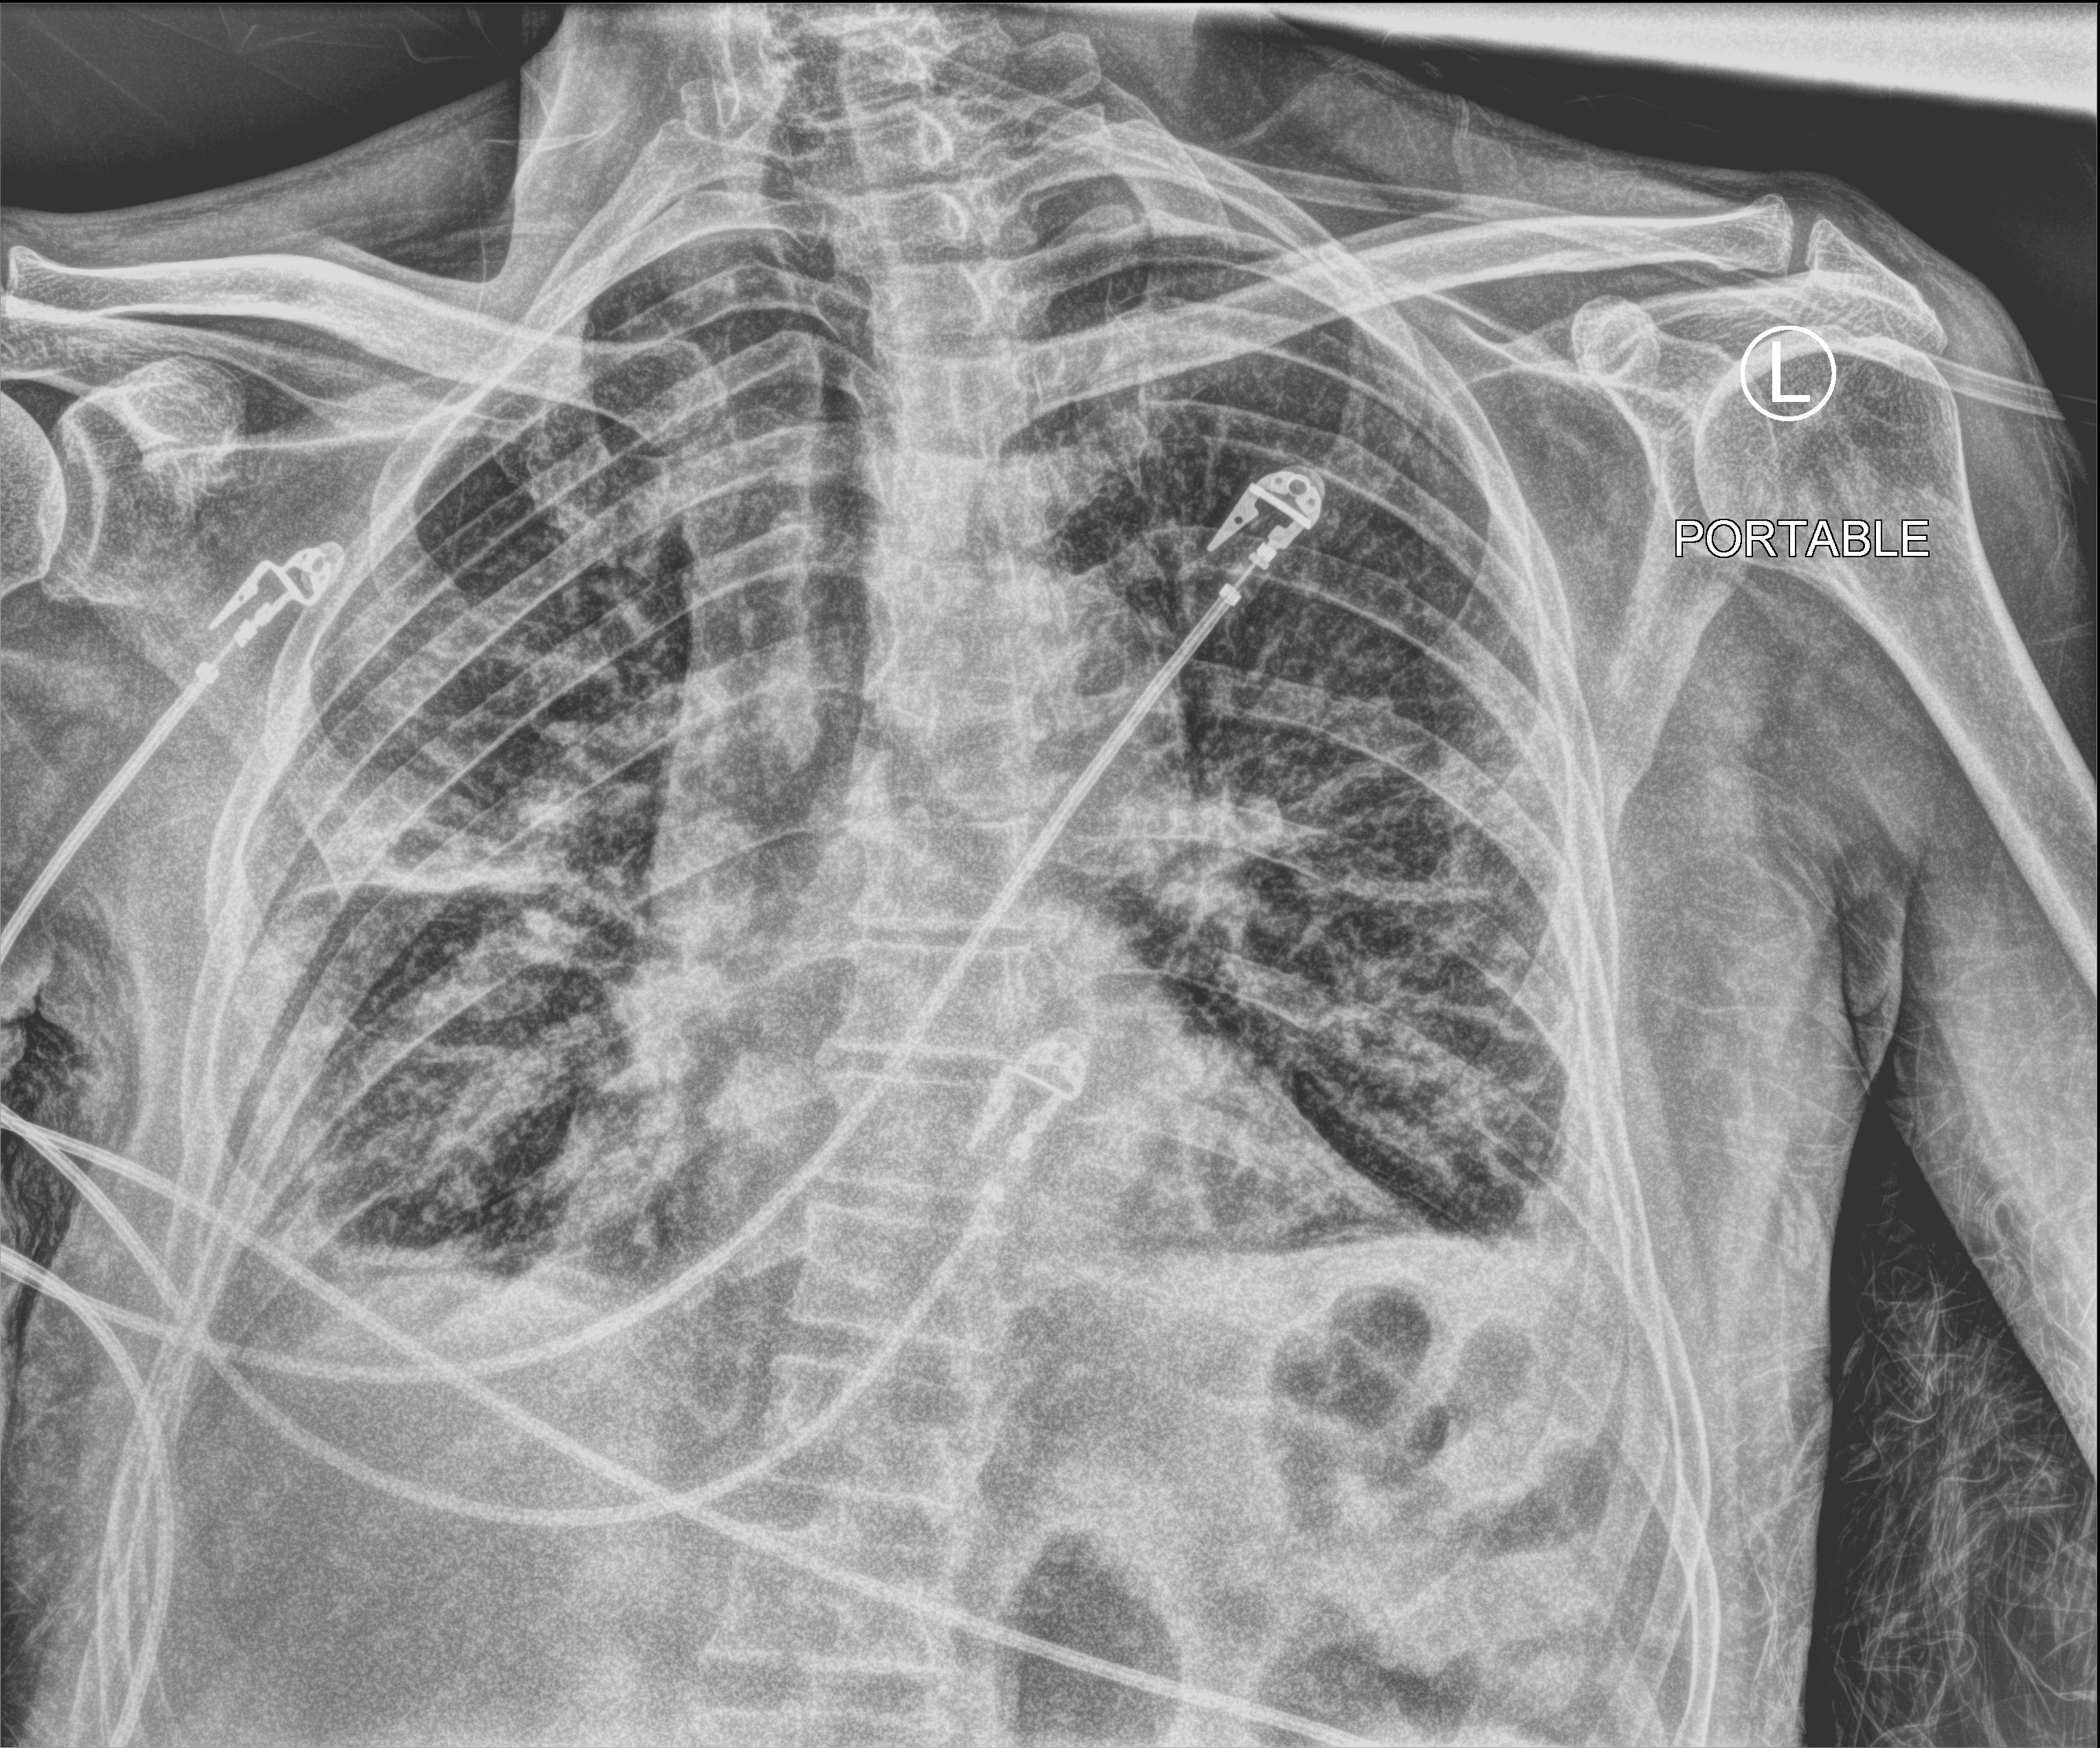
Bedside chest radiograph (computed radiography); anteroposterior (AP) projection. Patient hospitalised with COVID-19; male, aged 75–90 years.
From the hospital-stay record, not from the radiograph (when in the stay this image was taken is not recorded):
- admitted to intensive care during this hospital stay: yes
- mechanically ventilated during this hospital stay: yes
- hypertension (admission record): no